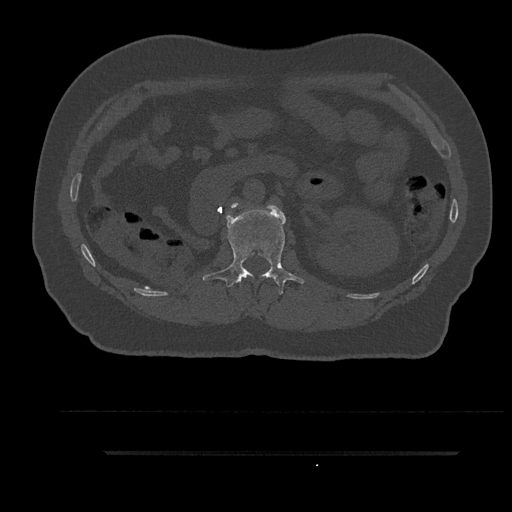
CT including the spine, one axial slice. Reconstruction kernel Br40s/3. 120 kVp. Bone window (W 1800 / L 400 HU). 0.5 mm slice thickness. 512 × 512 image matrix, field of view 432 × 432 mm. Male patient, age 63 years. From the clinical record (not read from this slice): primary cancer: renal; vertebrae with lytic lesions (as recorded): T8.
Structures marked on this image (semi-automatically segmented with operator editing):
- L1 vertebra: bounding box [x1, y1, x2, y2] px = [203, 205, 304, 295]
- L2 vertebra: [231, 203, 238, 208]